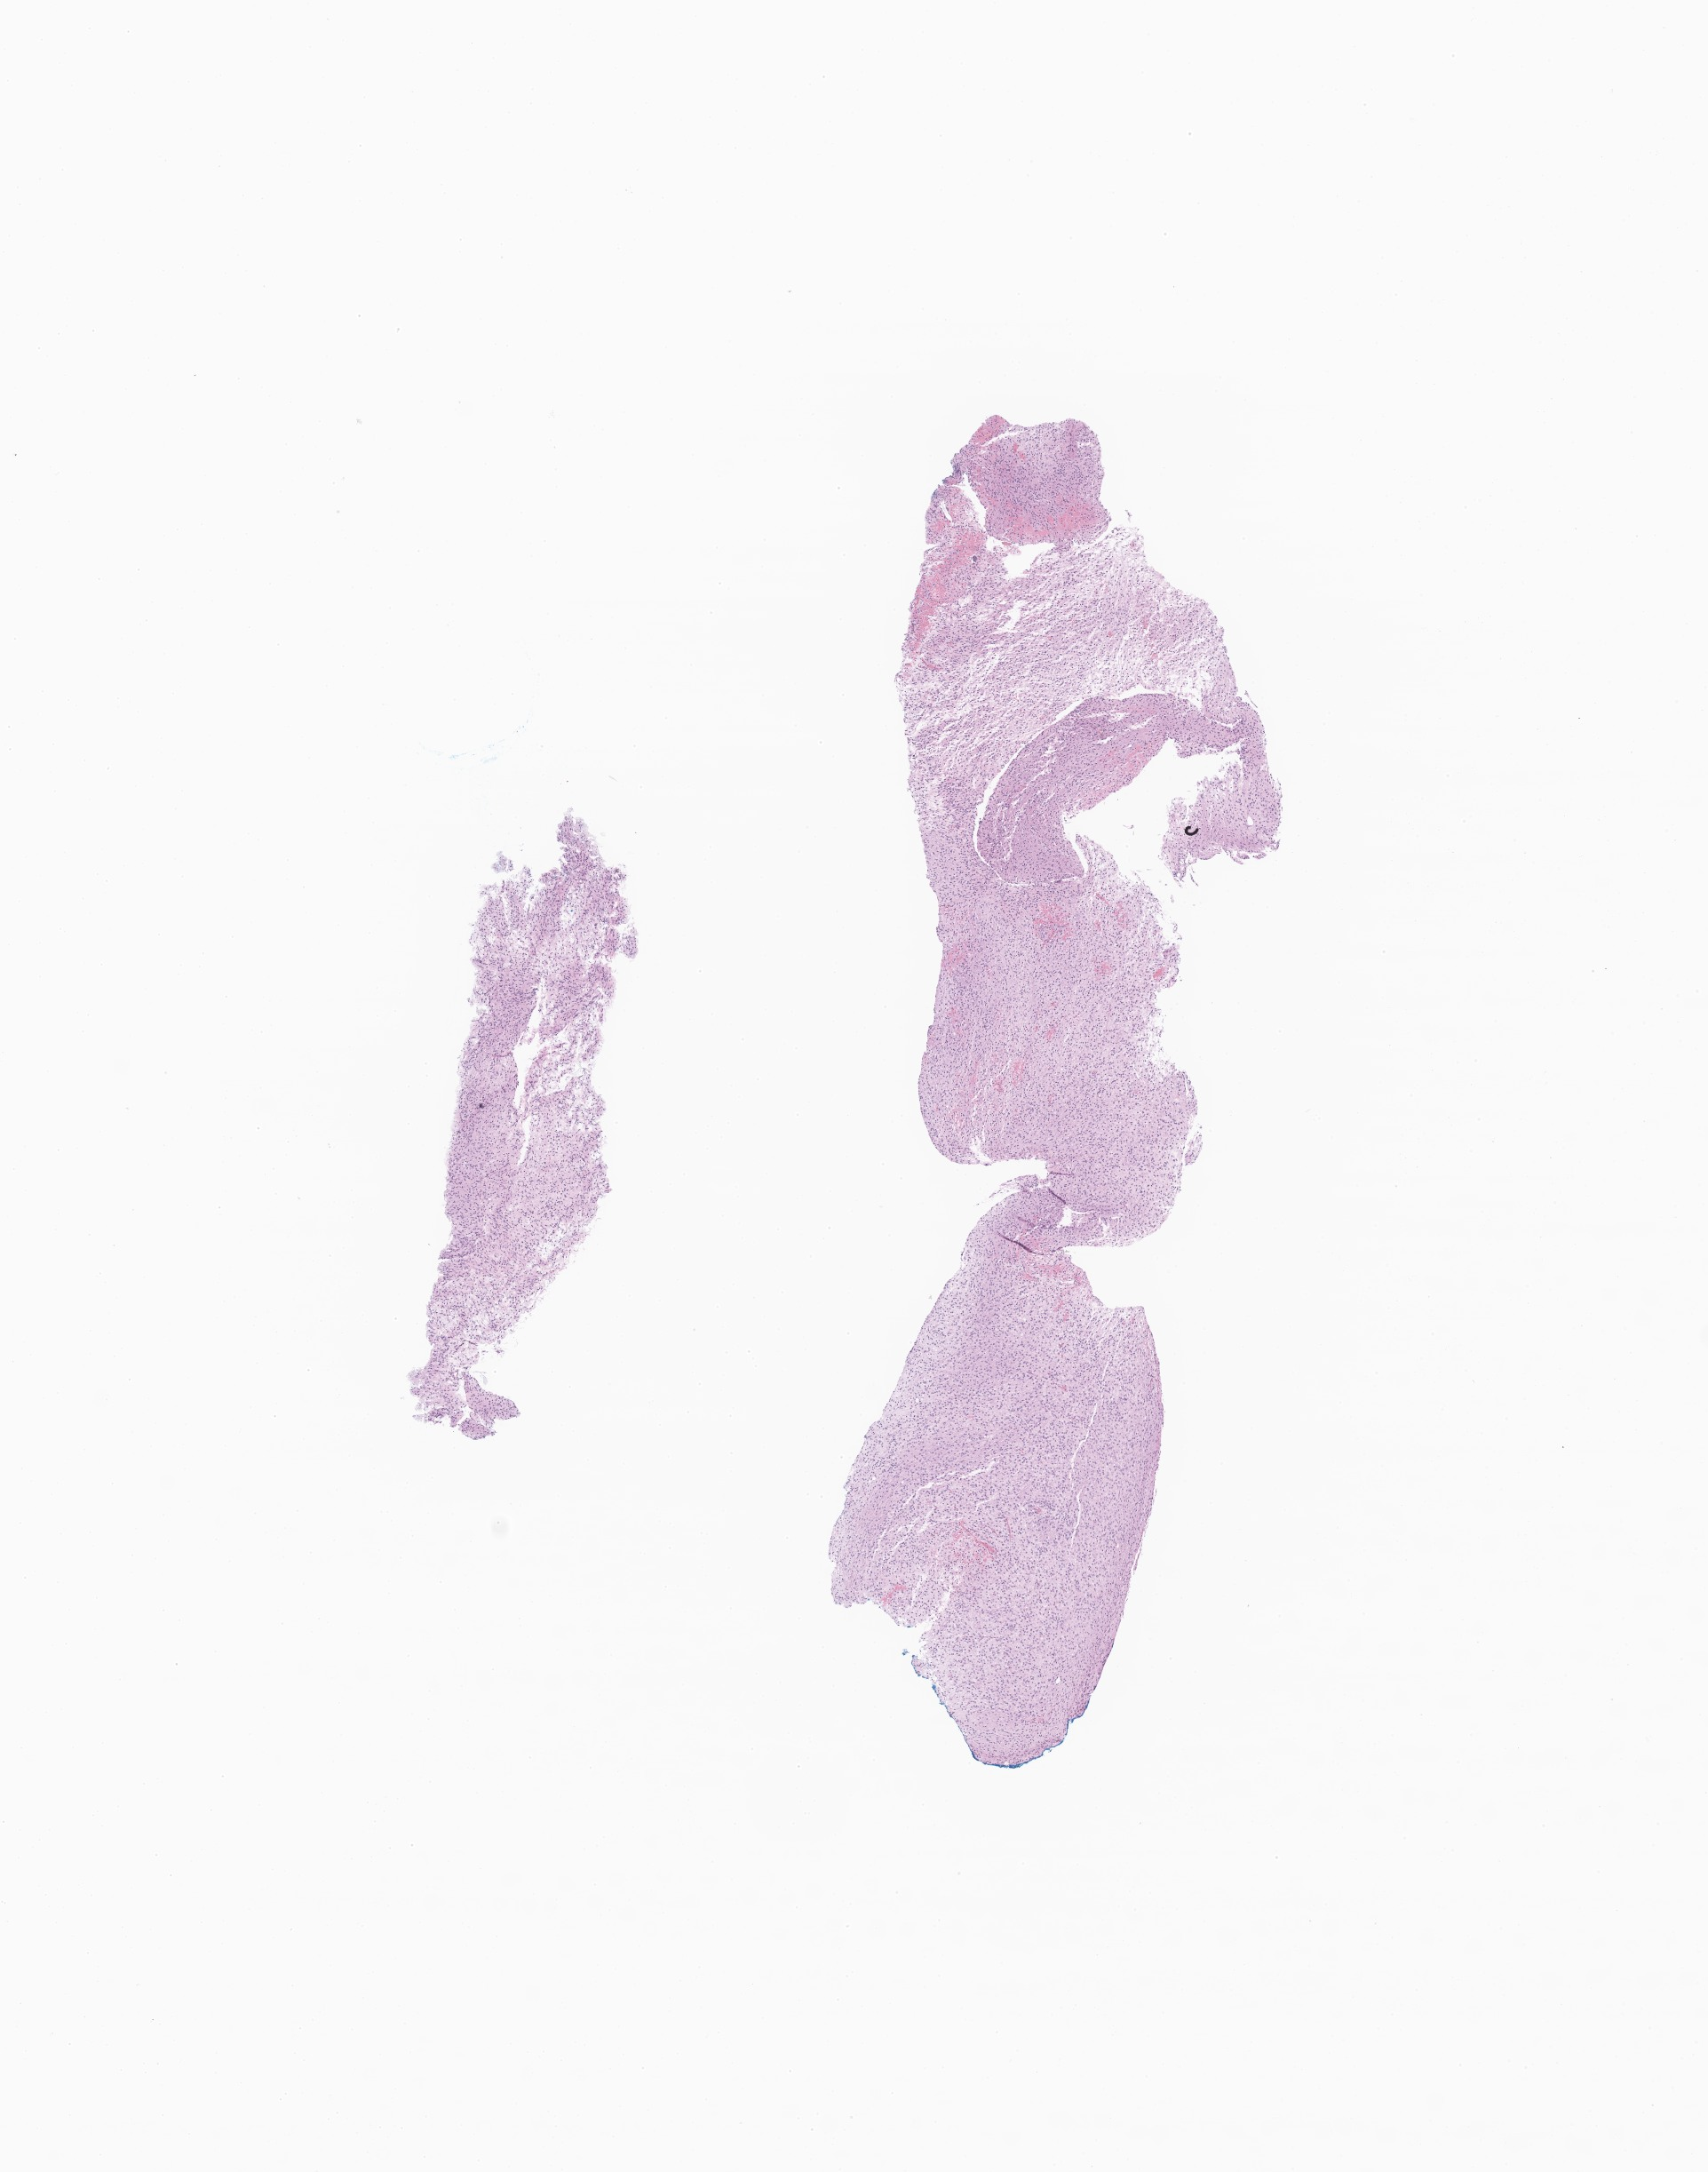
H&E whole-slide image of tumor tissue from the brain — low-resolution overview of the scanned area, about 8.1 x 10.3 mm. FFPE section. Female patient, age 203 months (16 years 11 months).
Recorded diagnosis: Glioma, malignant.